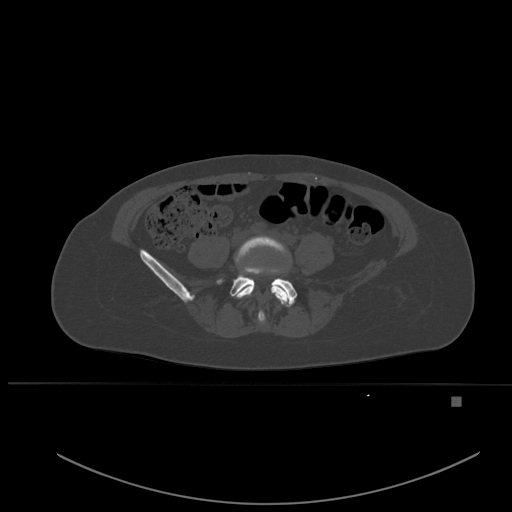
CT including the spine, one axial slice. Slice 162 of 651 in the series (ordered by position). Bone window (W 1800 / L 400 HU). 512 × 512 image matrix, field of view 443 × 443 mm. Patient: female, 49 years. Case-level facts recorded for this patient, not image findings: primary cancer: breast; vertebrae with lytic lesions (as recorded): L3, T12, L4.
Outlined on this slice (semi-automatic segmentation, software-assisted and operator-edited):
- L4 vertebra: box from (x=236, y=235) to (x=290, y=323) px
- L5 vertebra: (x=217, y=257)–(x=298, y=307)